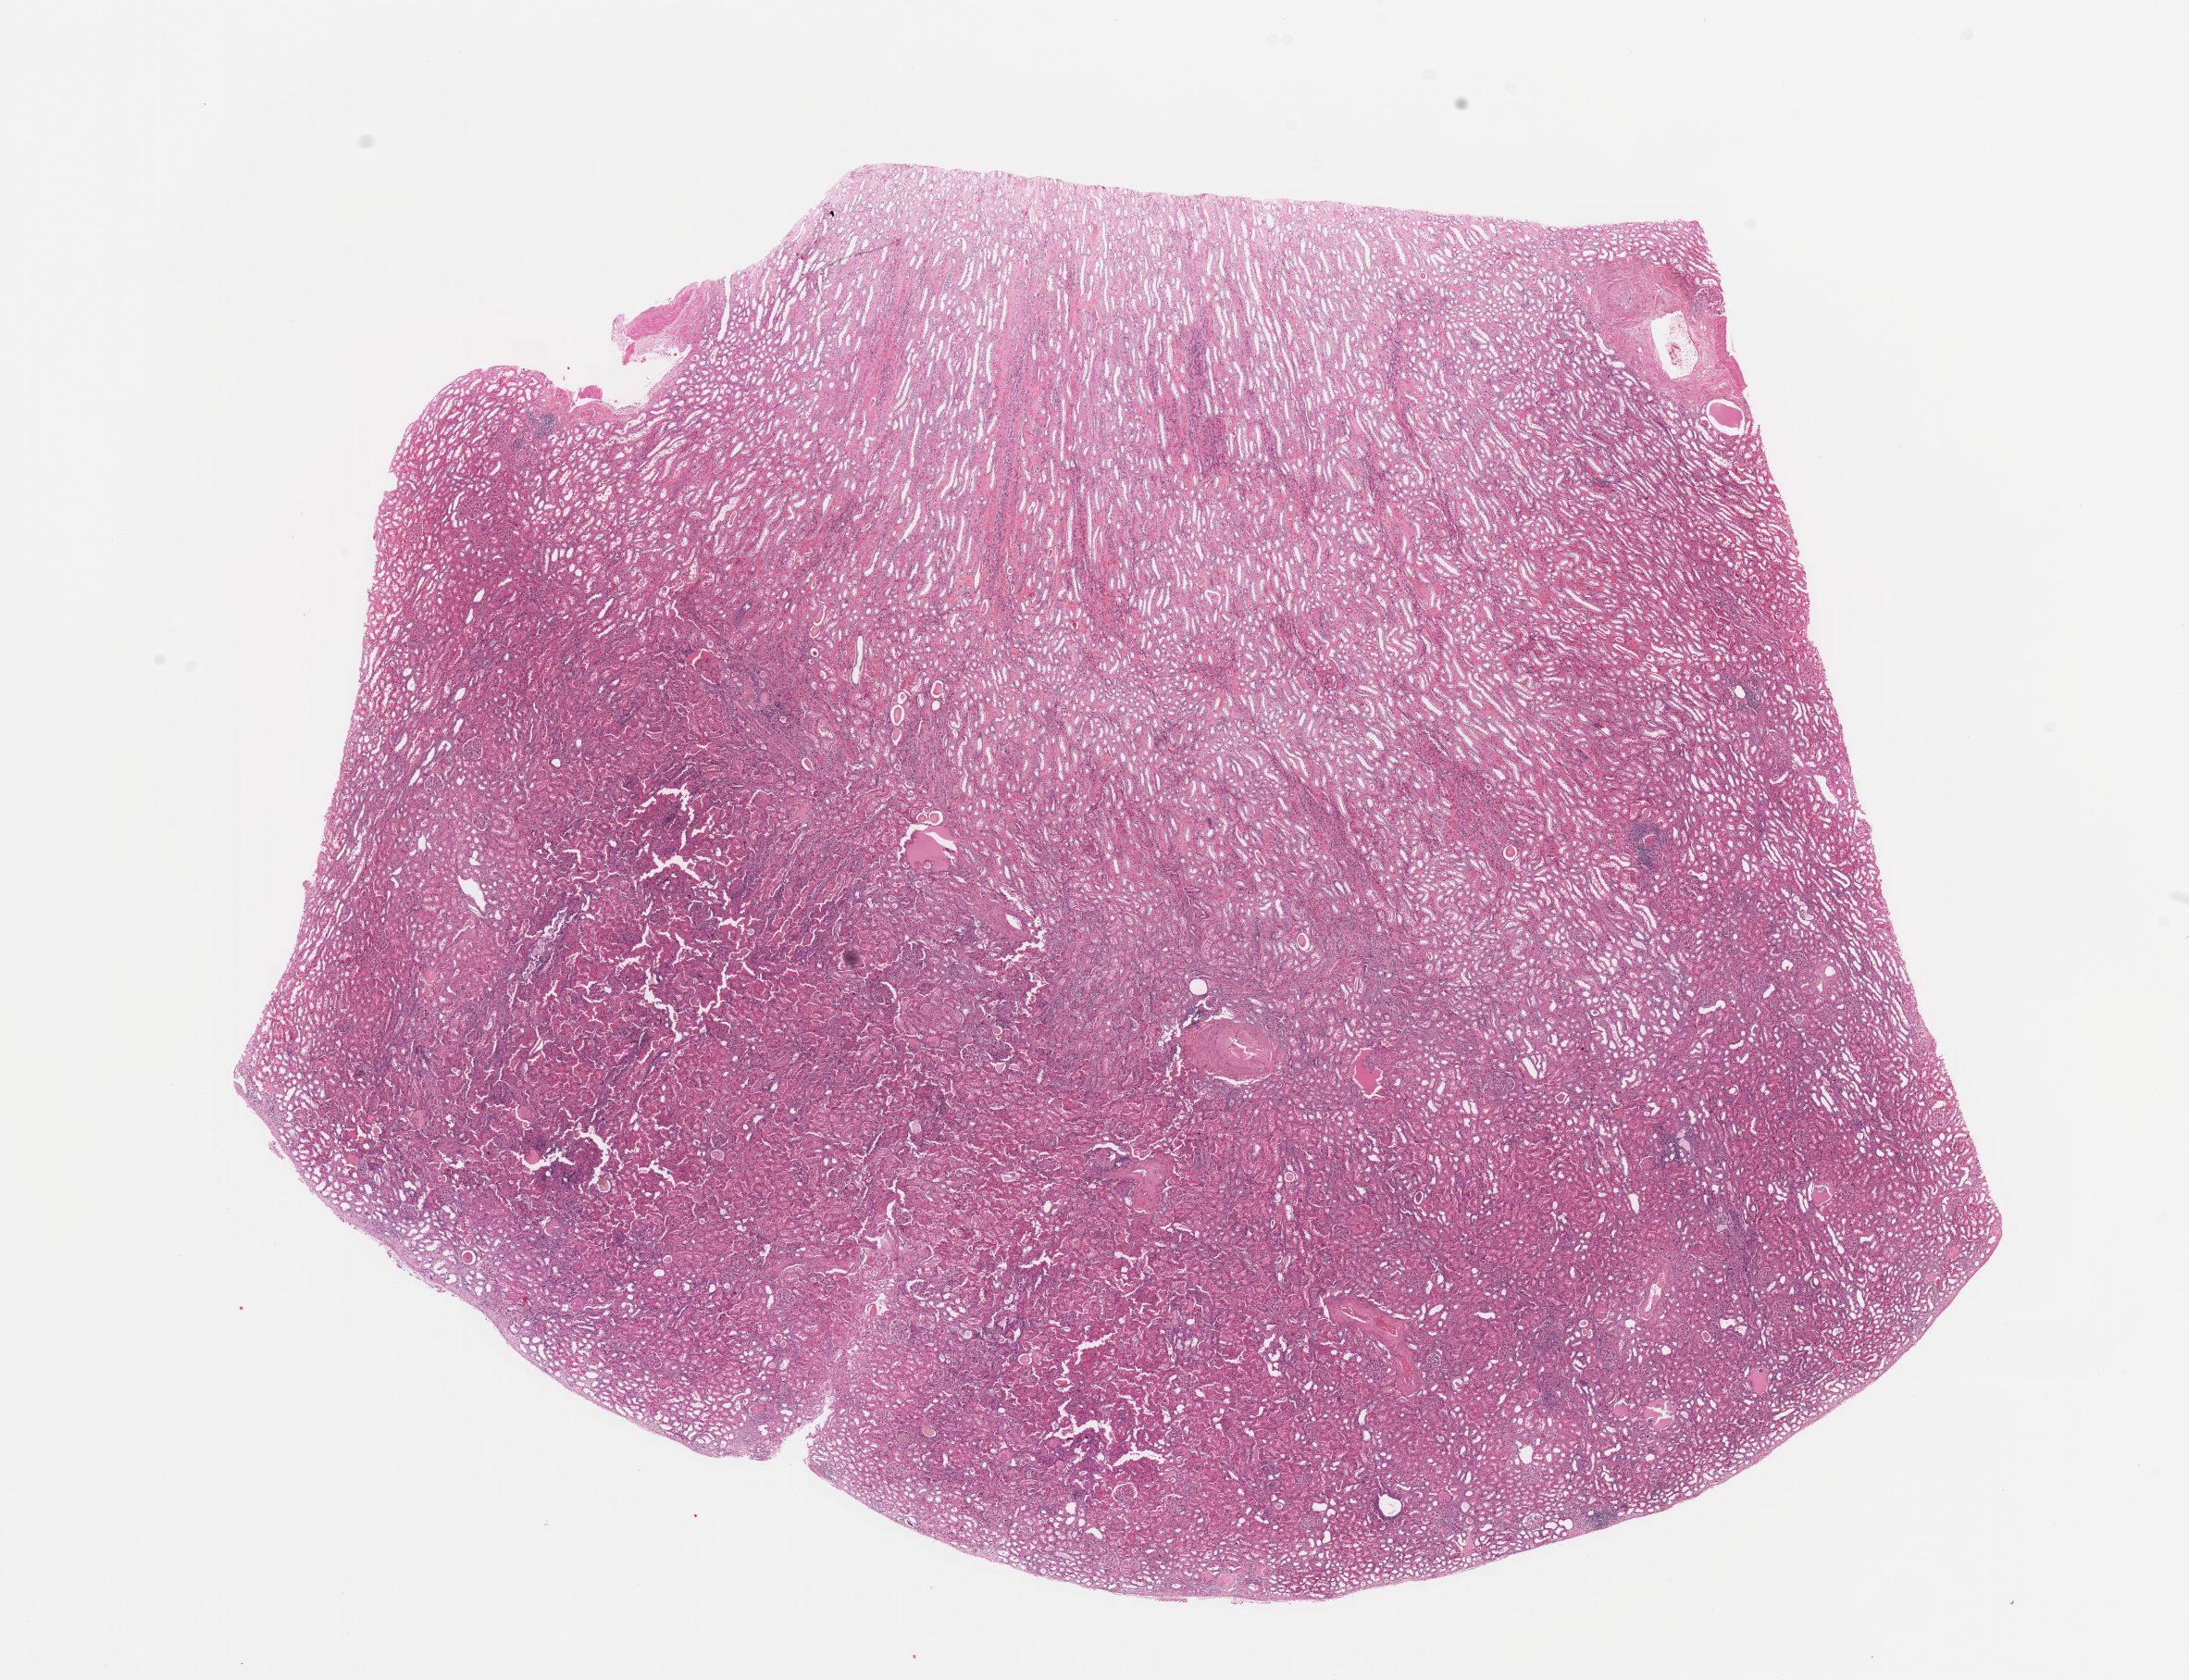
Whole-slide histology image, Hematoxylin and eosin (H&E) stained, low-resolution overview of the scanned area, about 18.7 x 14.4 mm. Normal (non-tumour) tissue sample, sampled site: kidney. Patient: male, age 70 years.
This section: normal (non-tumour) tissue from the same patient. Patient diagnosis: Renal cell carcinoma, NOS.